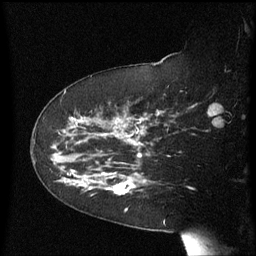
Breast MRI (dynamic contrast-enhanced), one sagittal slice; position 40 of 60 along the scan axis; dynamic contrast-enhanced series, image 2 of 3 at this slice position (ordered by acquisition); 1.5 T; TE 4.2 ms, TR 8.4 ms; 2.3 mm slice thickness; 256 × 256 image matrix, field of view 200 × 200 mm. Patient: female, 63 years. From the clinical record (not read from this slice): setting: breast cancer imaged before/during neoadjuvant chemotherapy; receptor status: HER2-positive.
Annotated regions visible in this slice (semi-automatically segmented with operator editing):
- analysis volume of interest (the breast-tissue region the enhancement analysis was run in; not a lesion): bounding box [x1, y1, x2, y2] px = [63, 144, 147, 195]
- tumour enhancement mask (voxels above the 70 % enhancement threshold inside the analysis volume of interest): [63, 144, 142, 194]